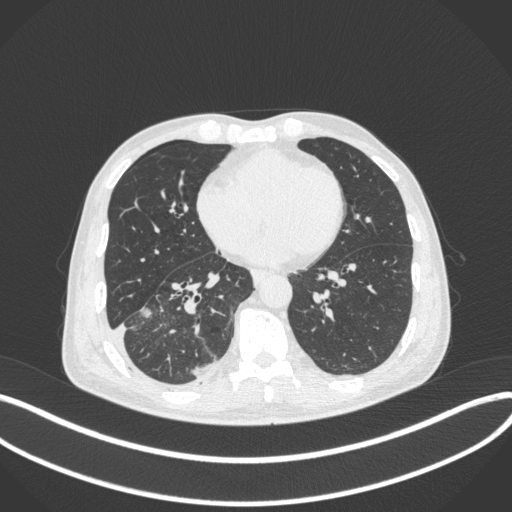
Chest CT, one axial slice; slice 150 of 385 in the series (ordered by position); reconstruction kernel B31f; lung window (W 1500 / L -600 HU); 1 mm slice thickness; 512 × 512 image matrix, field of view 400 × 400 mm. Patient: male, 64 years. From the clinical record (not read from this slice): clinical TNM (as recorded): T3 N0 M0.
Annotated regions visible in this slice (bounding box drawn by a radiologist):
- lung tumour (recorded histology: adenocarcinoma): bounding box [x1, y1, x2, y2] px = [137, 301, 157, 321]